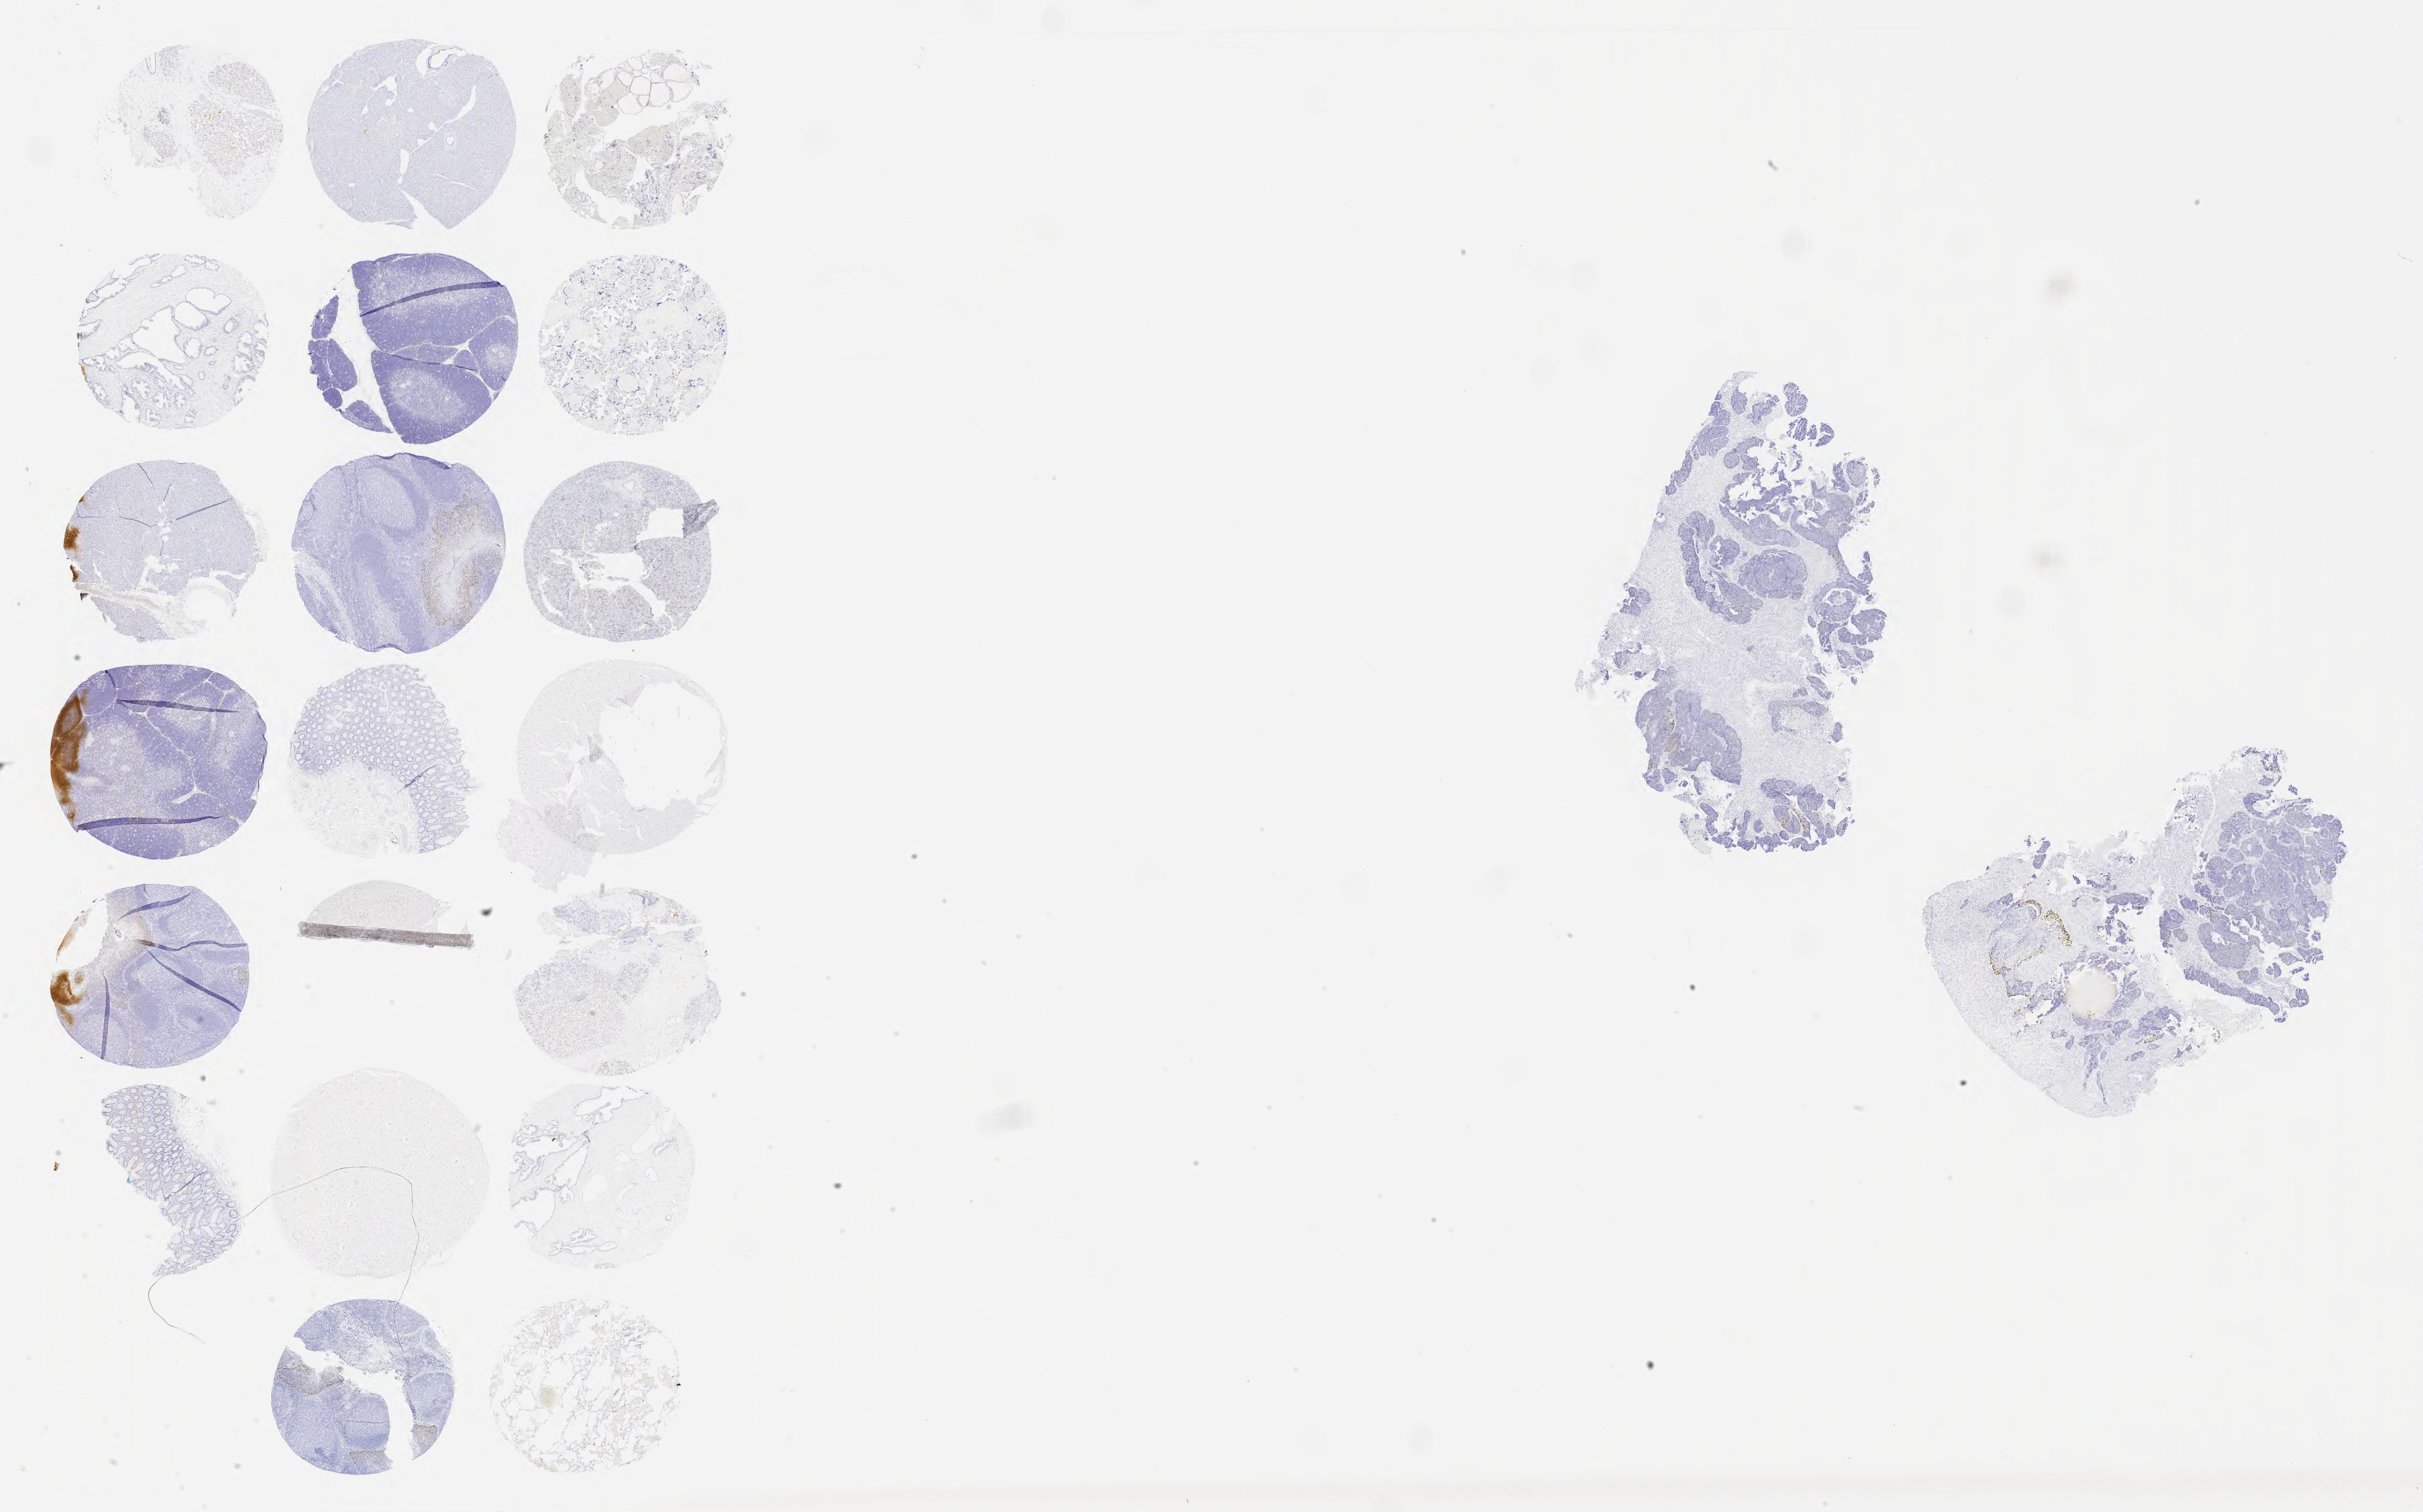
Immunohistochemistry (IHC) whole-slide image stained for p63 — low-resolution overview of the scanned area, about 29.7 x 18.5 mm. Specimen: tumor tissue. Site: cervix. Patient female; age 38 years.
Diagnosis: Squamous cell carcinoma, large cell, nonkeratinizing, NOS.